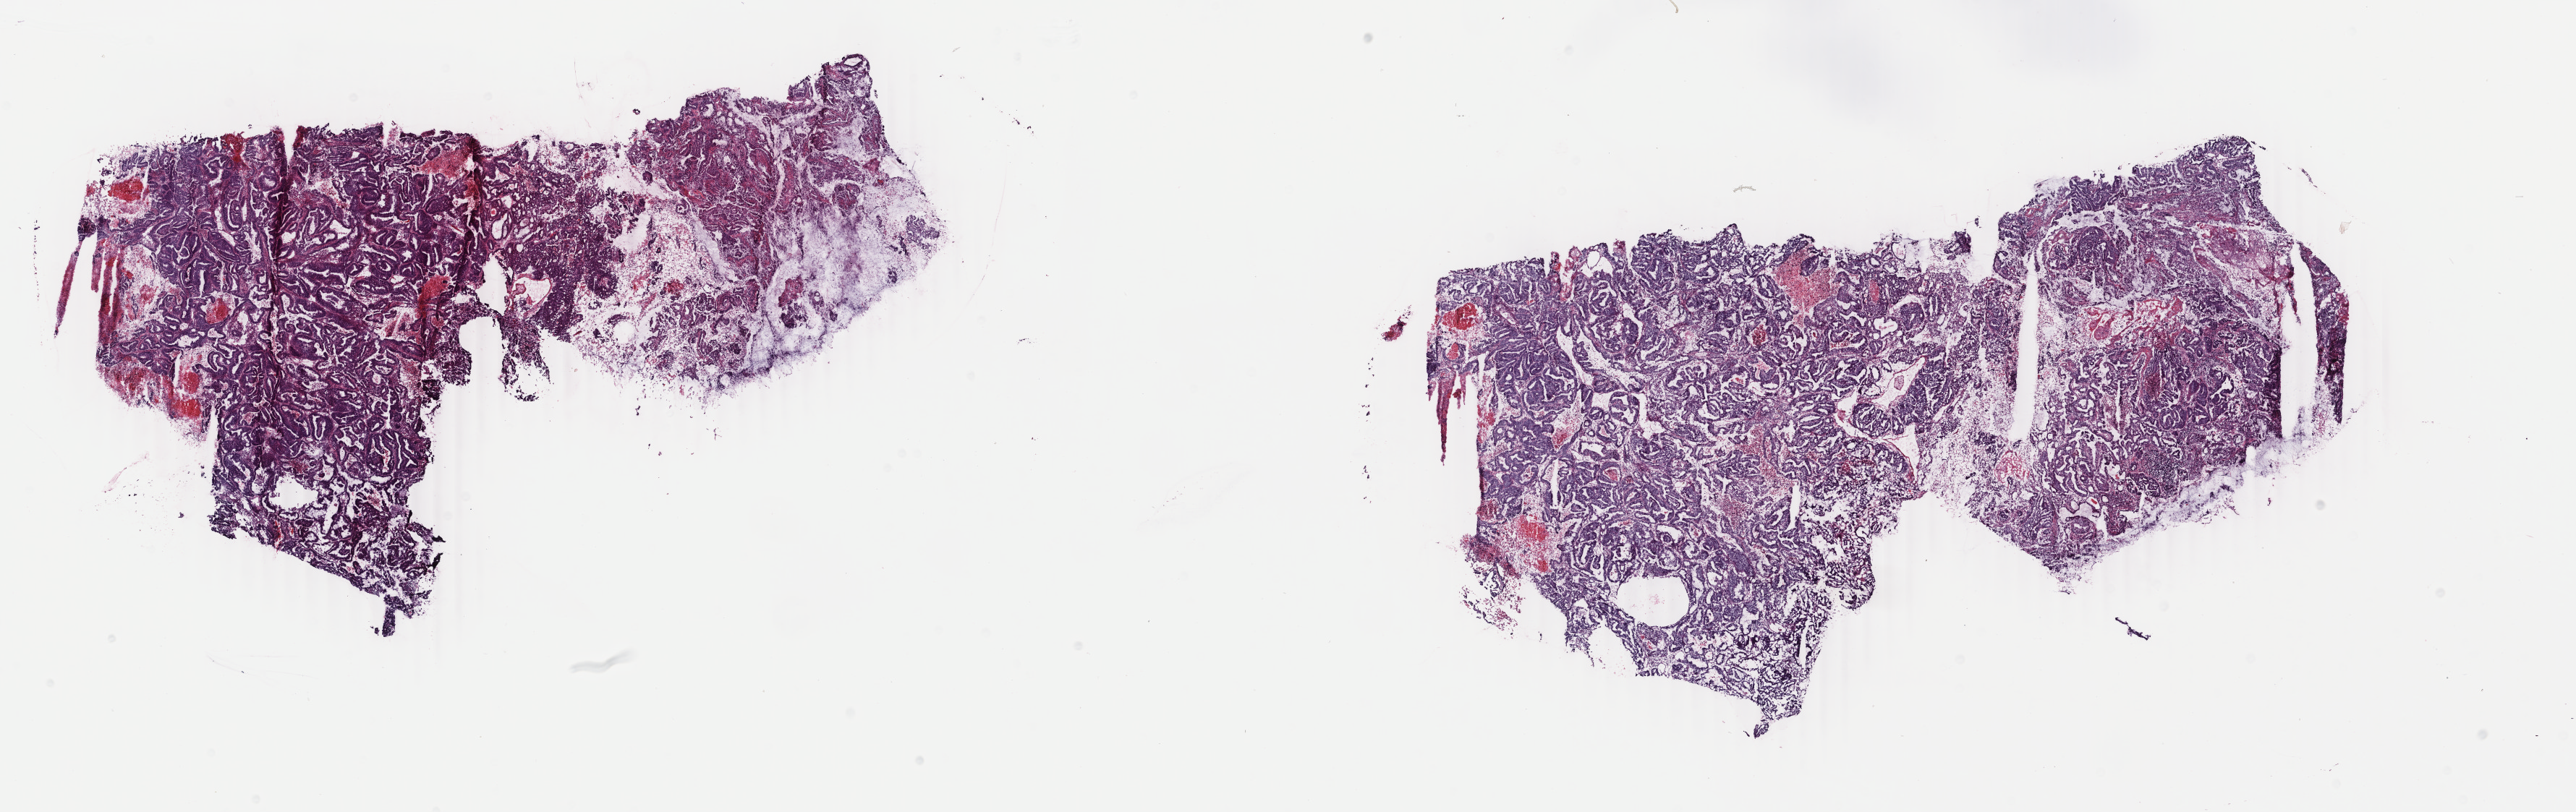
Digitized Hematoxylin and eosin (H&E) stained tissue section (whole slide), shown as a low-resolution overview of the whole scanned area (about 28.3 x 8.9 mm). Frozen section from the bottom of the tissue portion. Sample: primary tumour, uterus. Female patient; age at initial diagnosis 71 years.
Histologic diagnosis: Endometrioid adenocarcinoma, NOS.